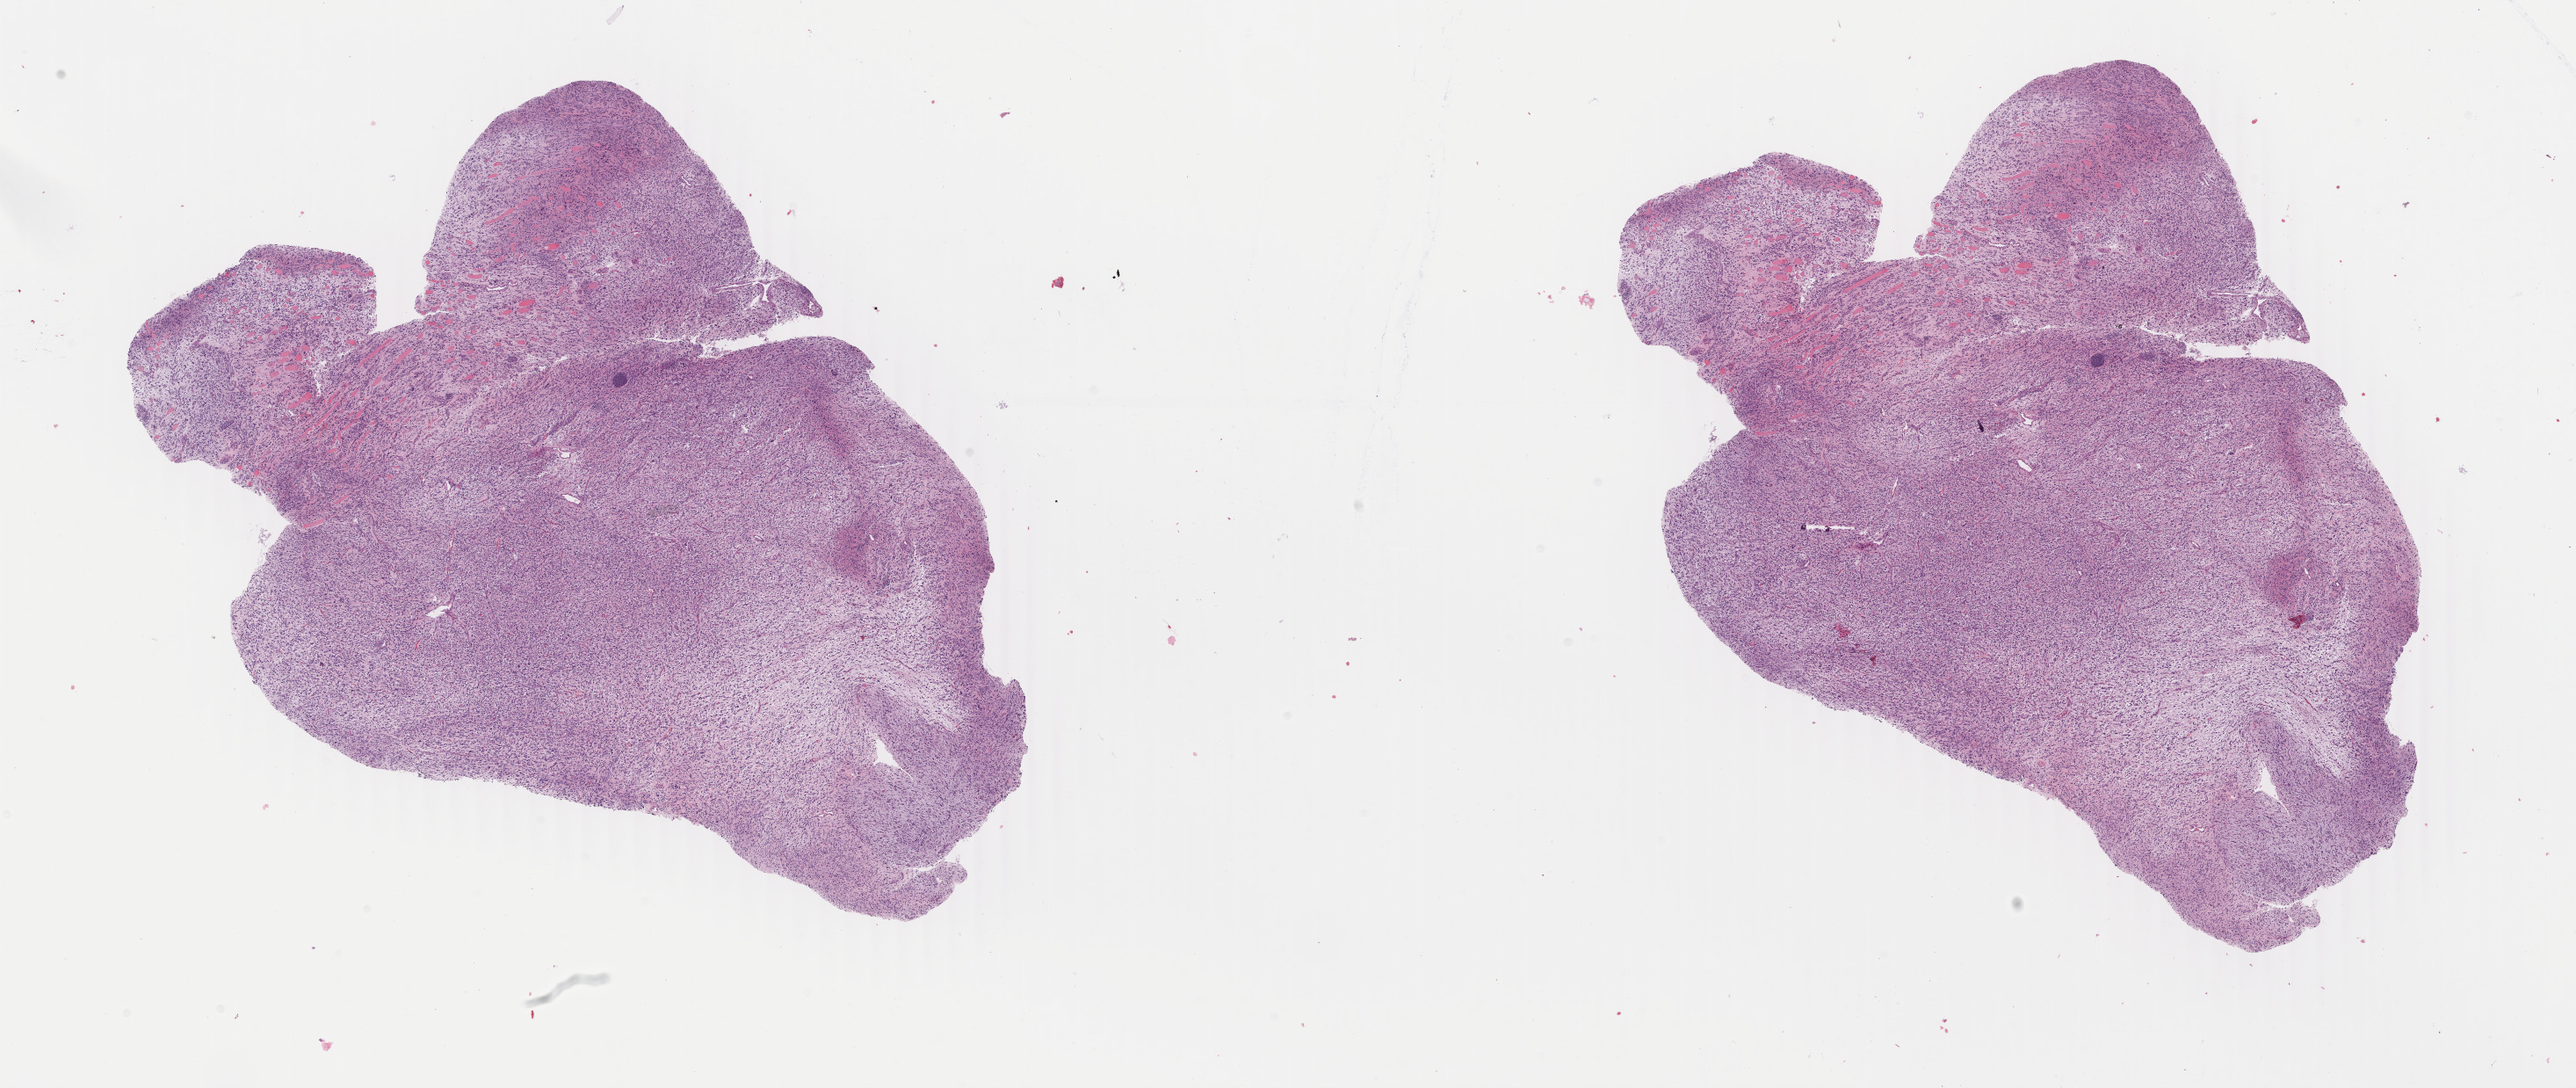
Whole-slide histology image, H&E — whole scanned area (about 23.3 x 9.8 mm) shown as a low-resolution overview, FFPE section, sample: primary tumour, connective, subcutaneous and other soft tissues. Patient: female, age at initial diagnosis 84 years.
Diagnosis: Giant cell sarcoma (connective, subcutaneous and other soft tissues of lower limb and hip).